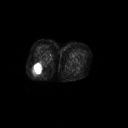
FDG PET of an extremity soft-tissue mass (from a PET/CT study), one axial slice. Position 29 of 267 along the scan axis. 3.27 mm slice thickness. 128 × 128 image matrix. Patient: female, 70 years. From the clinical record (not read from this slice): histological type: synovial sarcoma; grade: intermediate; site of the primary tumour: right buttock.
Outlined on this slice (expert contour drawn on MRI and transferred to this co-registered scan by the dataset authors):
- gross tumour volume including surrounding oedema: bounding box <33,61,41,73> (left, top, right, bottom; pixels)
- gross tumour volume (mass): <33,63,41,73>